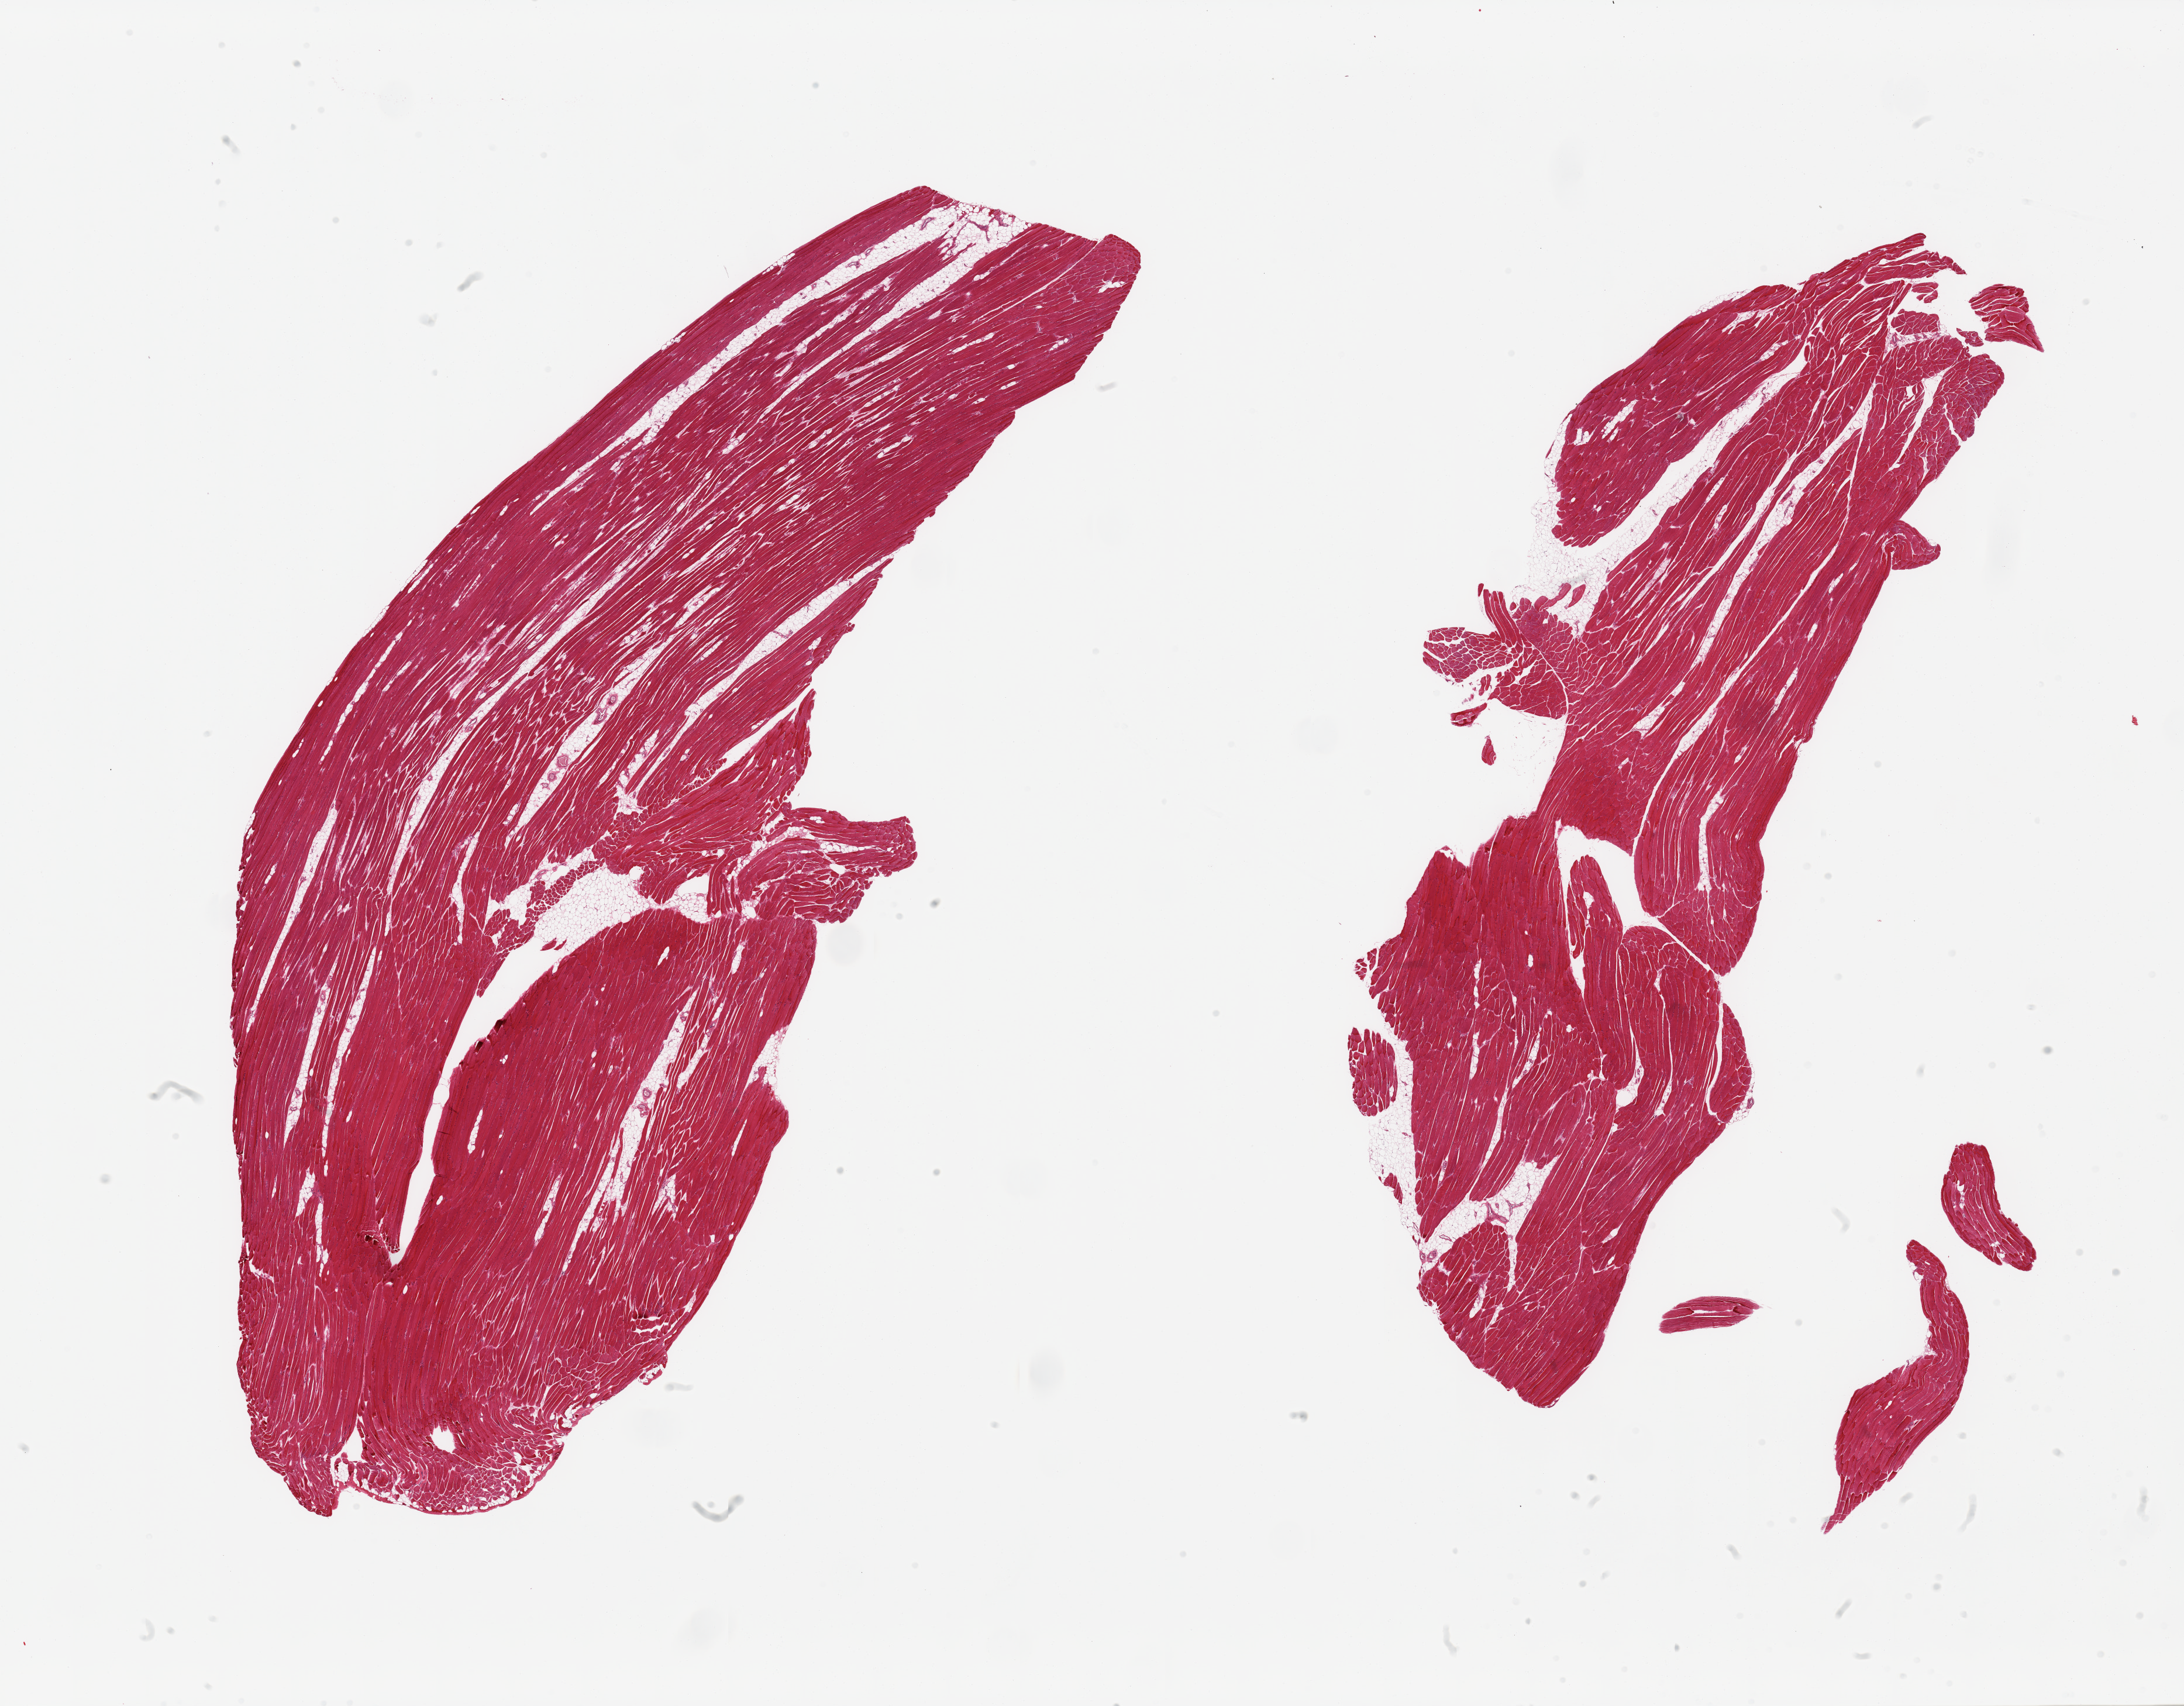
Digitized H&E-stained section, a low-resolution overview of the entire scanned area, about 29.5 x 23.1 mm (from a 20x scan); PAXgene-fixed paraffin-embedded (PFPE) section; section of skeletal muscle (target tissue); tissue donor sample. Donor: male.
- pathologist's review note for this sample: 2 pieces, ~10-15% interstitial fat